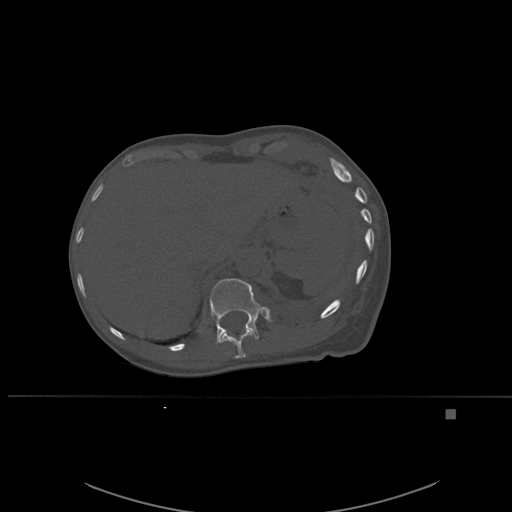
CT including the spine, one axial slice; bone window (W 1800 / L 400 HU); 1.5 mm slice thickness; 512 × 512 image matrix, field of view 440 × 440 mm. Female patient, age 45 years. Case-level facts recorded for this patient, not image findings: primary cancer: lung.
Structures marked on this image (semi-automatic segmentation, software-assisted and operator-edited):
- T11 vertebra: box from (x=220, y=328) to (x=254, y=359) px
- T12 vertebra: (x=210, y=278)–(x=262, y=344)